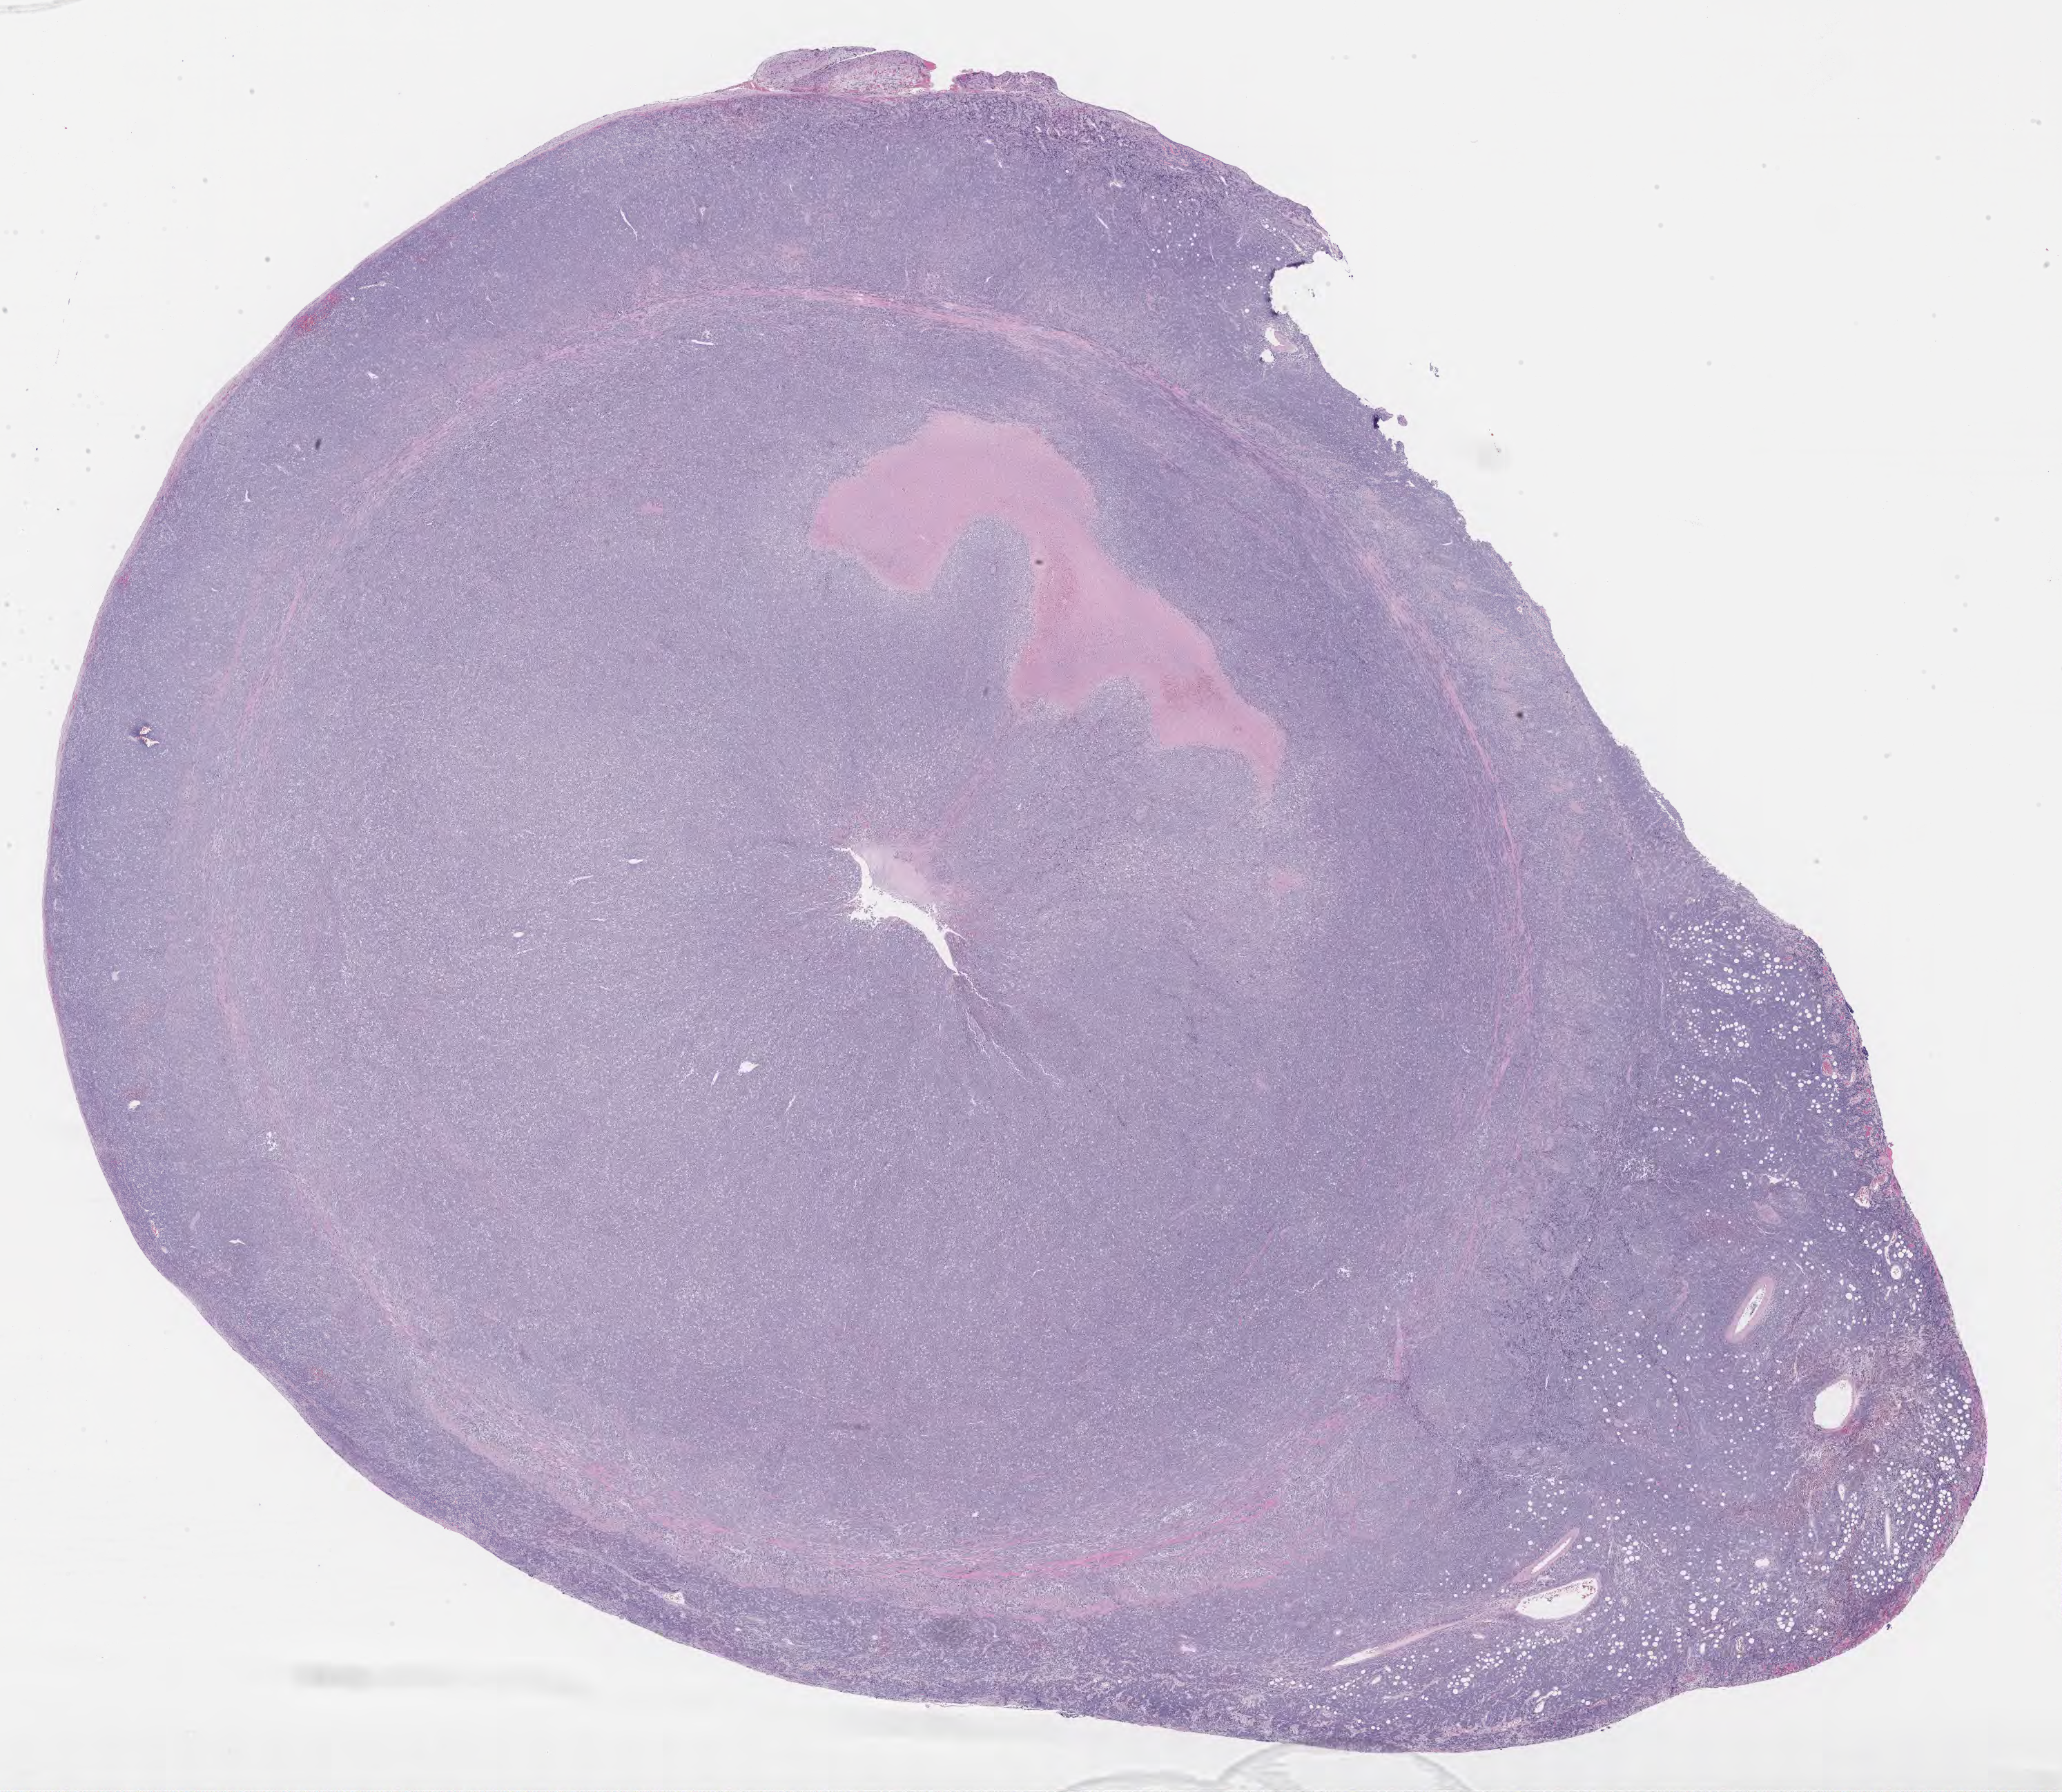
Hematoxylin and eosin (H&E) whole-slide image, a low-resolution overview of the entire scanned area, about 24.2 x 21.0 mm; specimen: tumor tissue; site: appendix. Patient: male, 20 years old.
Diagnosis: Burkitt lymphoma, NOS.